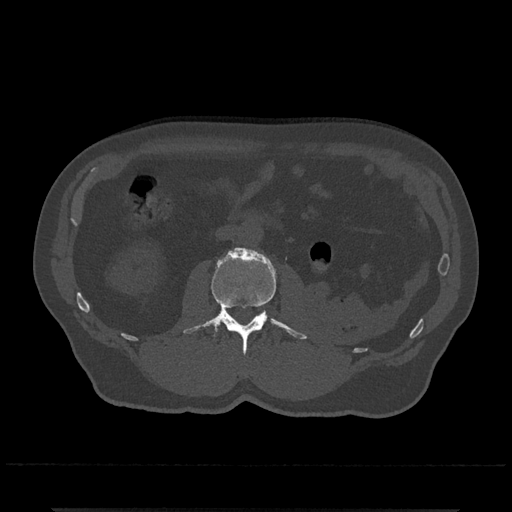
CT including the spine, one axial slice. Position 287 of 797 along the scan axis. Bone window (W 1800 / L 400 HU). 0.5 mm slice thickness. 512 × 512 image matrix. Patient: male, 67 years. From the clinical record (not read from this slice): primary cancer: prostate.
Structures marked on this image (semi-automatic segmentation, software-assisted and operator-edited):
- L2 vertebra: bounding box [x1, y1, x2, y2] px = [183, 248, 307, 354]